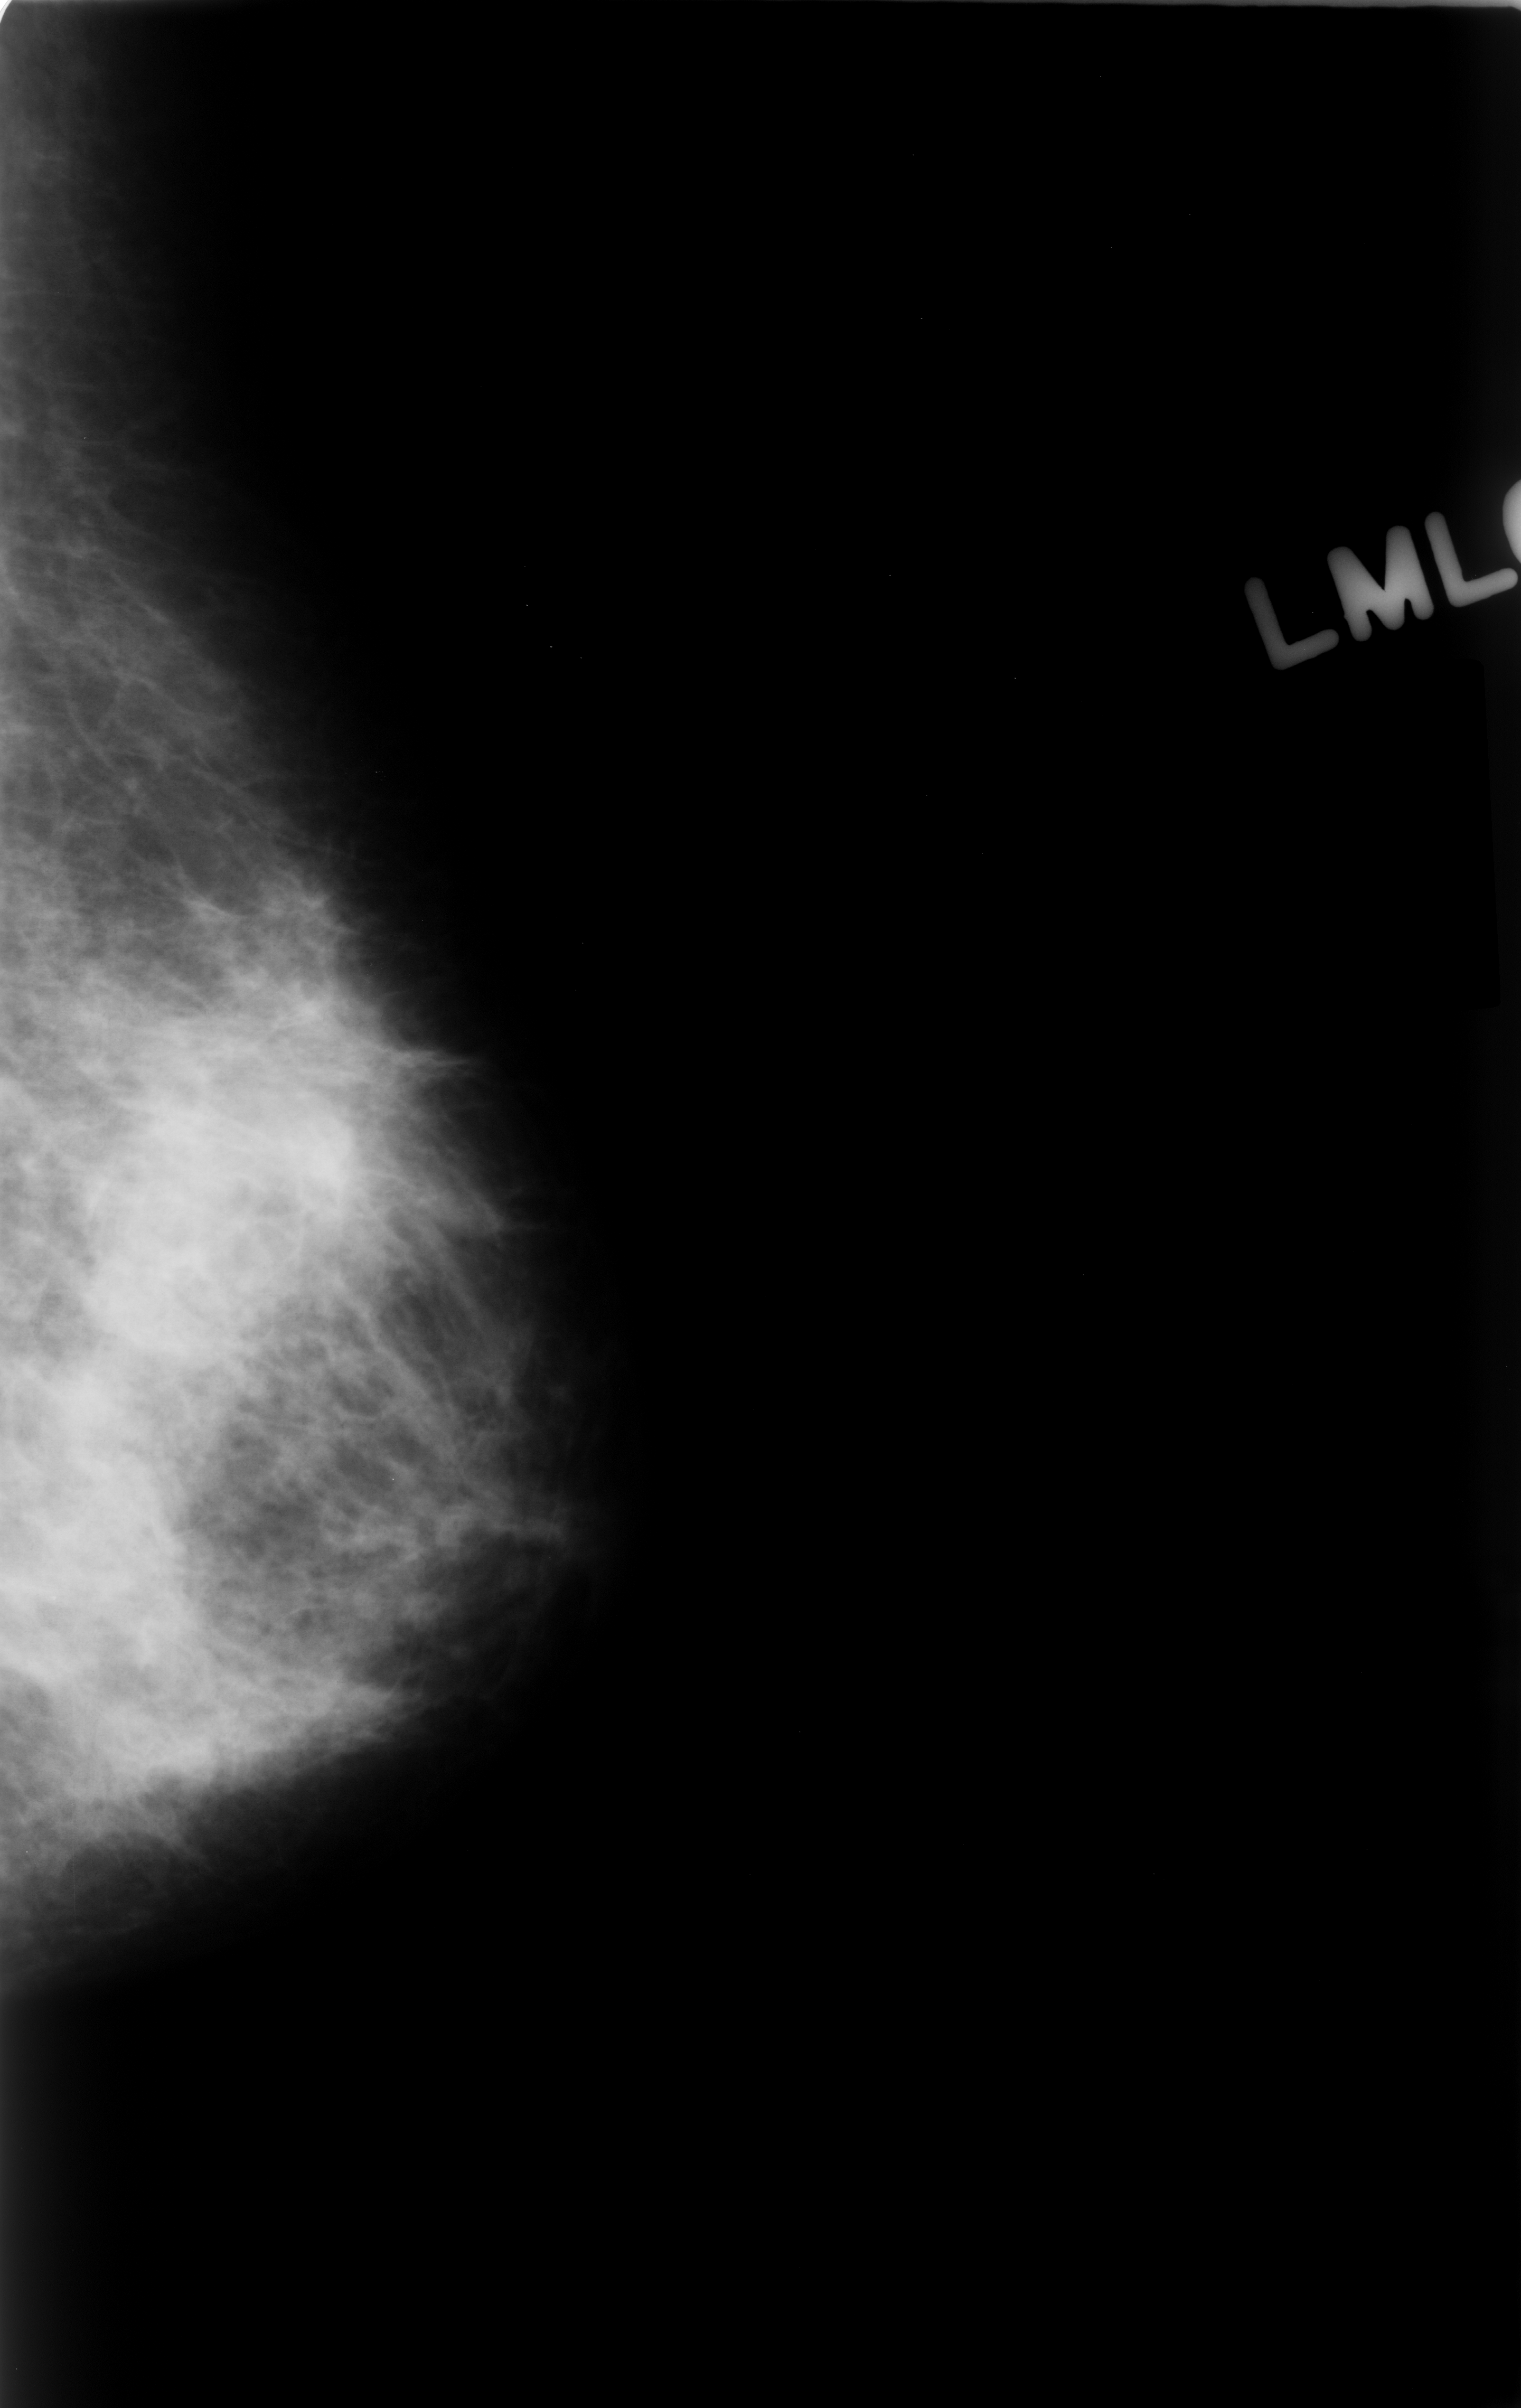
Scanned film-screen mammogram; left breast; MLO view; breast composition: heterogeneously dense (BI-RADS density category 3 of 4).
Radiologist-marked abnormalities on this image: mass, shape architectural distortion, margins ill defined; BI-RADS assessment category 5; subtlety rating 4 on a 1 (subtle) to 5 (obvious) scale; pathology result (as recorded, not read from the image): malignant.